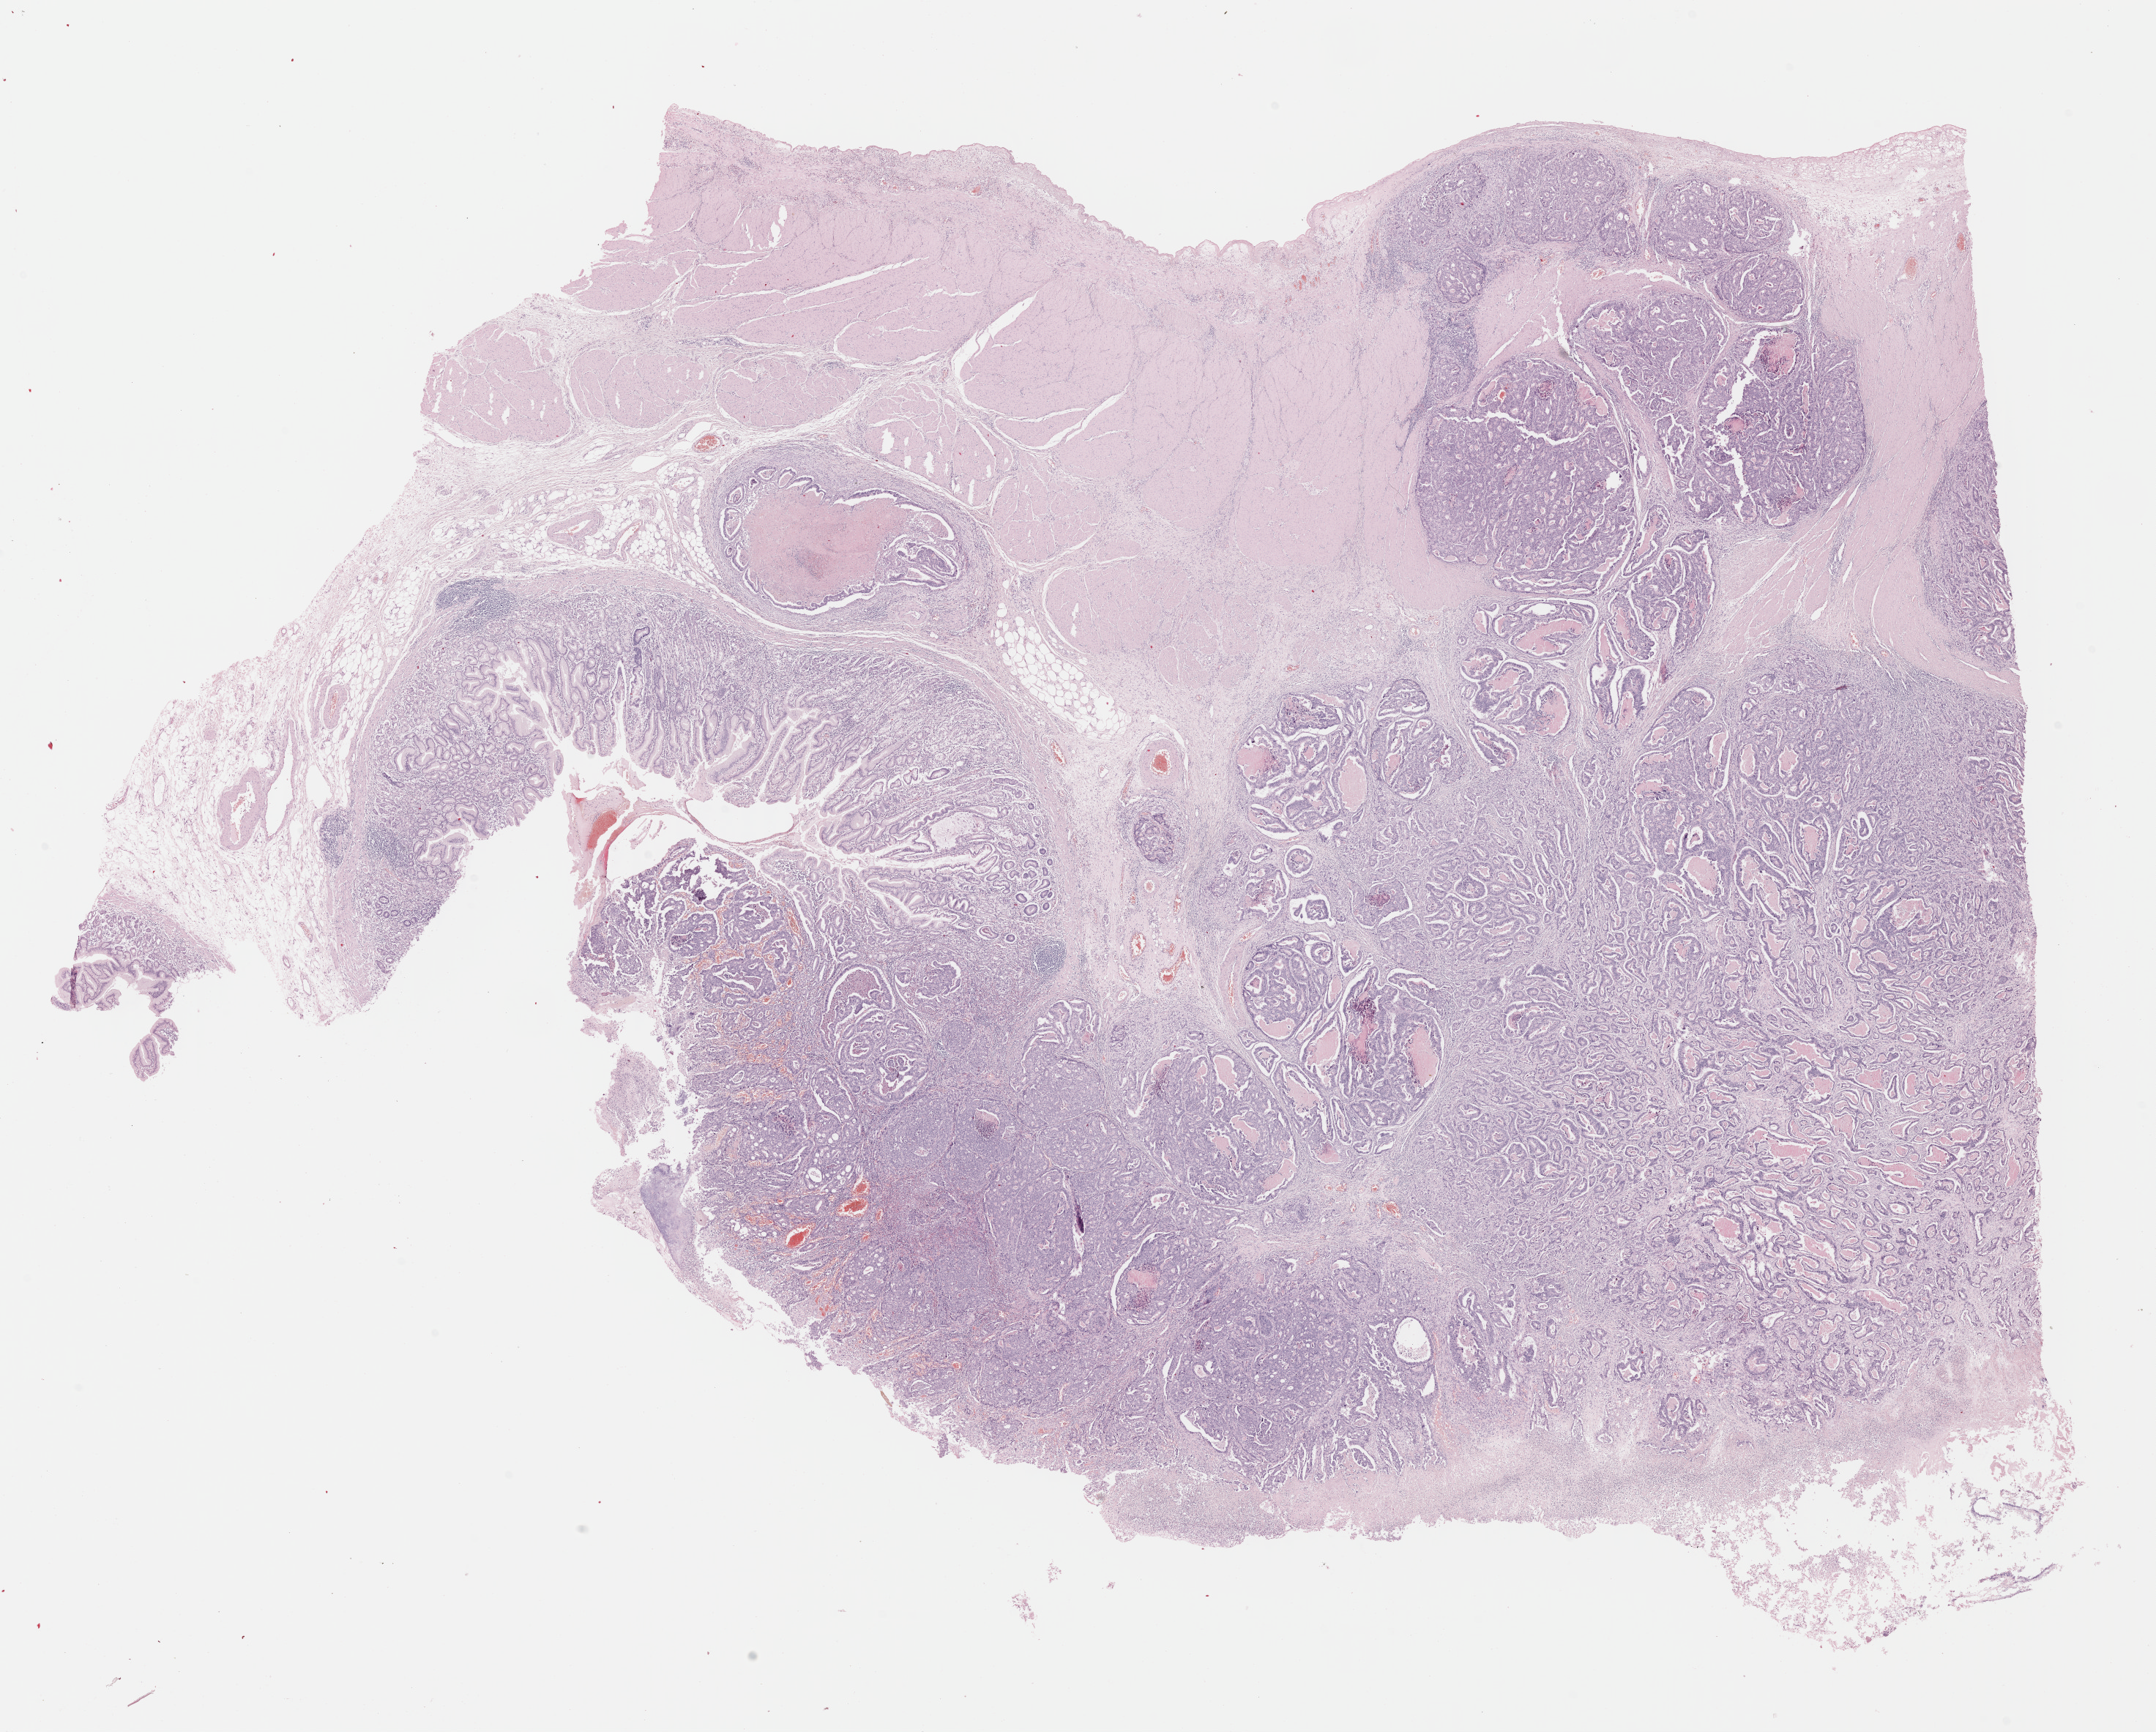
Digitized Hematoxylin and eosin (H&E) stained tissue section (whole slide) — whole scanned area (about 23.1 x 18.6 mm, from a 40x scan) shown as a low-resolution overview. Formalin-fixed paraffin-embedded (FFPE) diagnostic section. Stomach, primary tumour sample. Female patient; age at initial diagnosis 70 years. Histologic grade: G2 (moderately differentiated).
Lymph nodes positive (case pathology): 0 of 26 examined. AJCC pathologic stage: IB. TNM: T2 N0 M0. Pathologic diagnosis: Tubular adenocarcinoma.